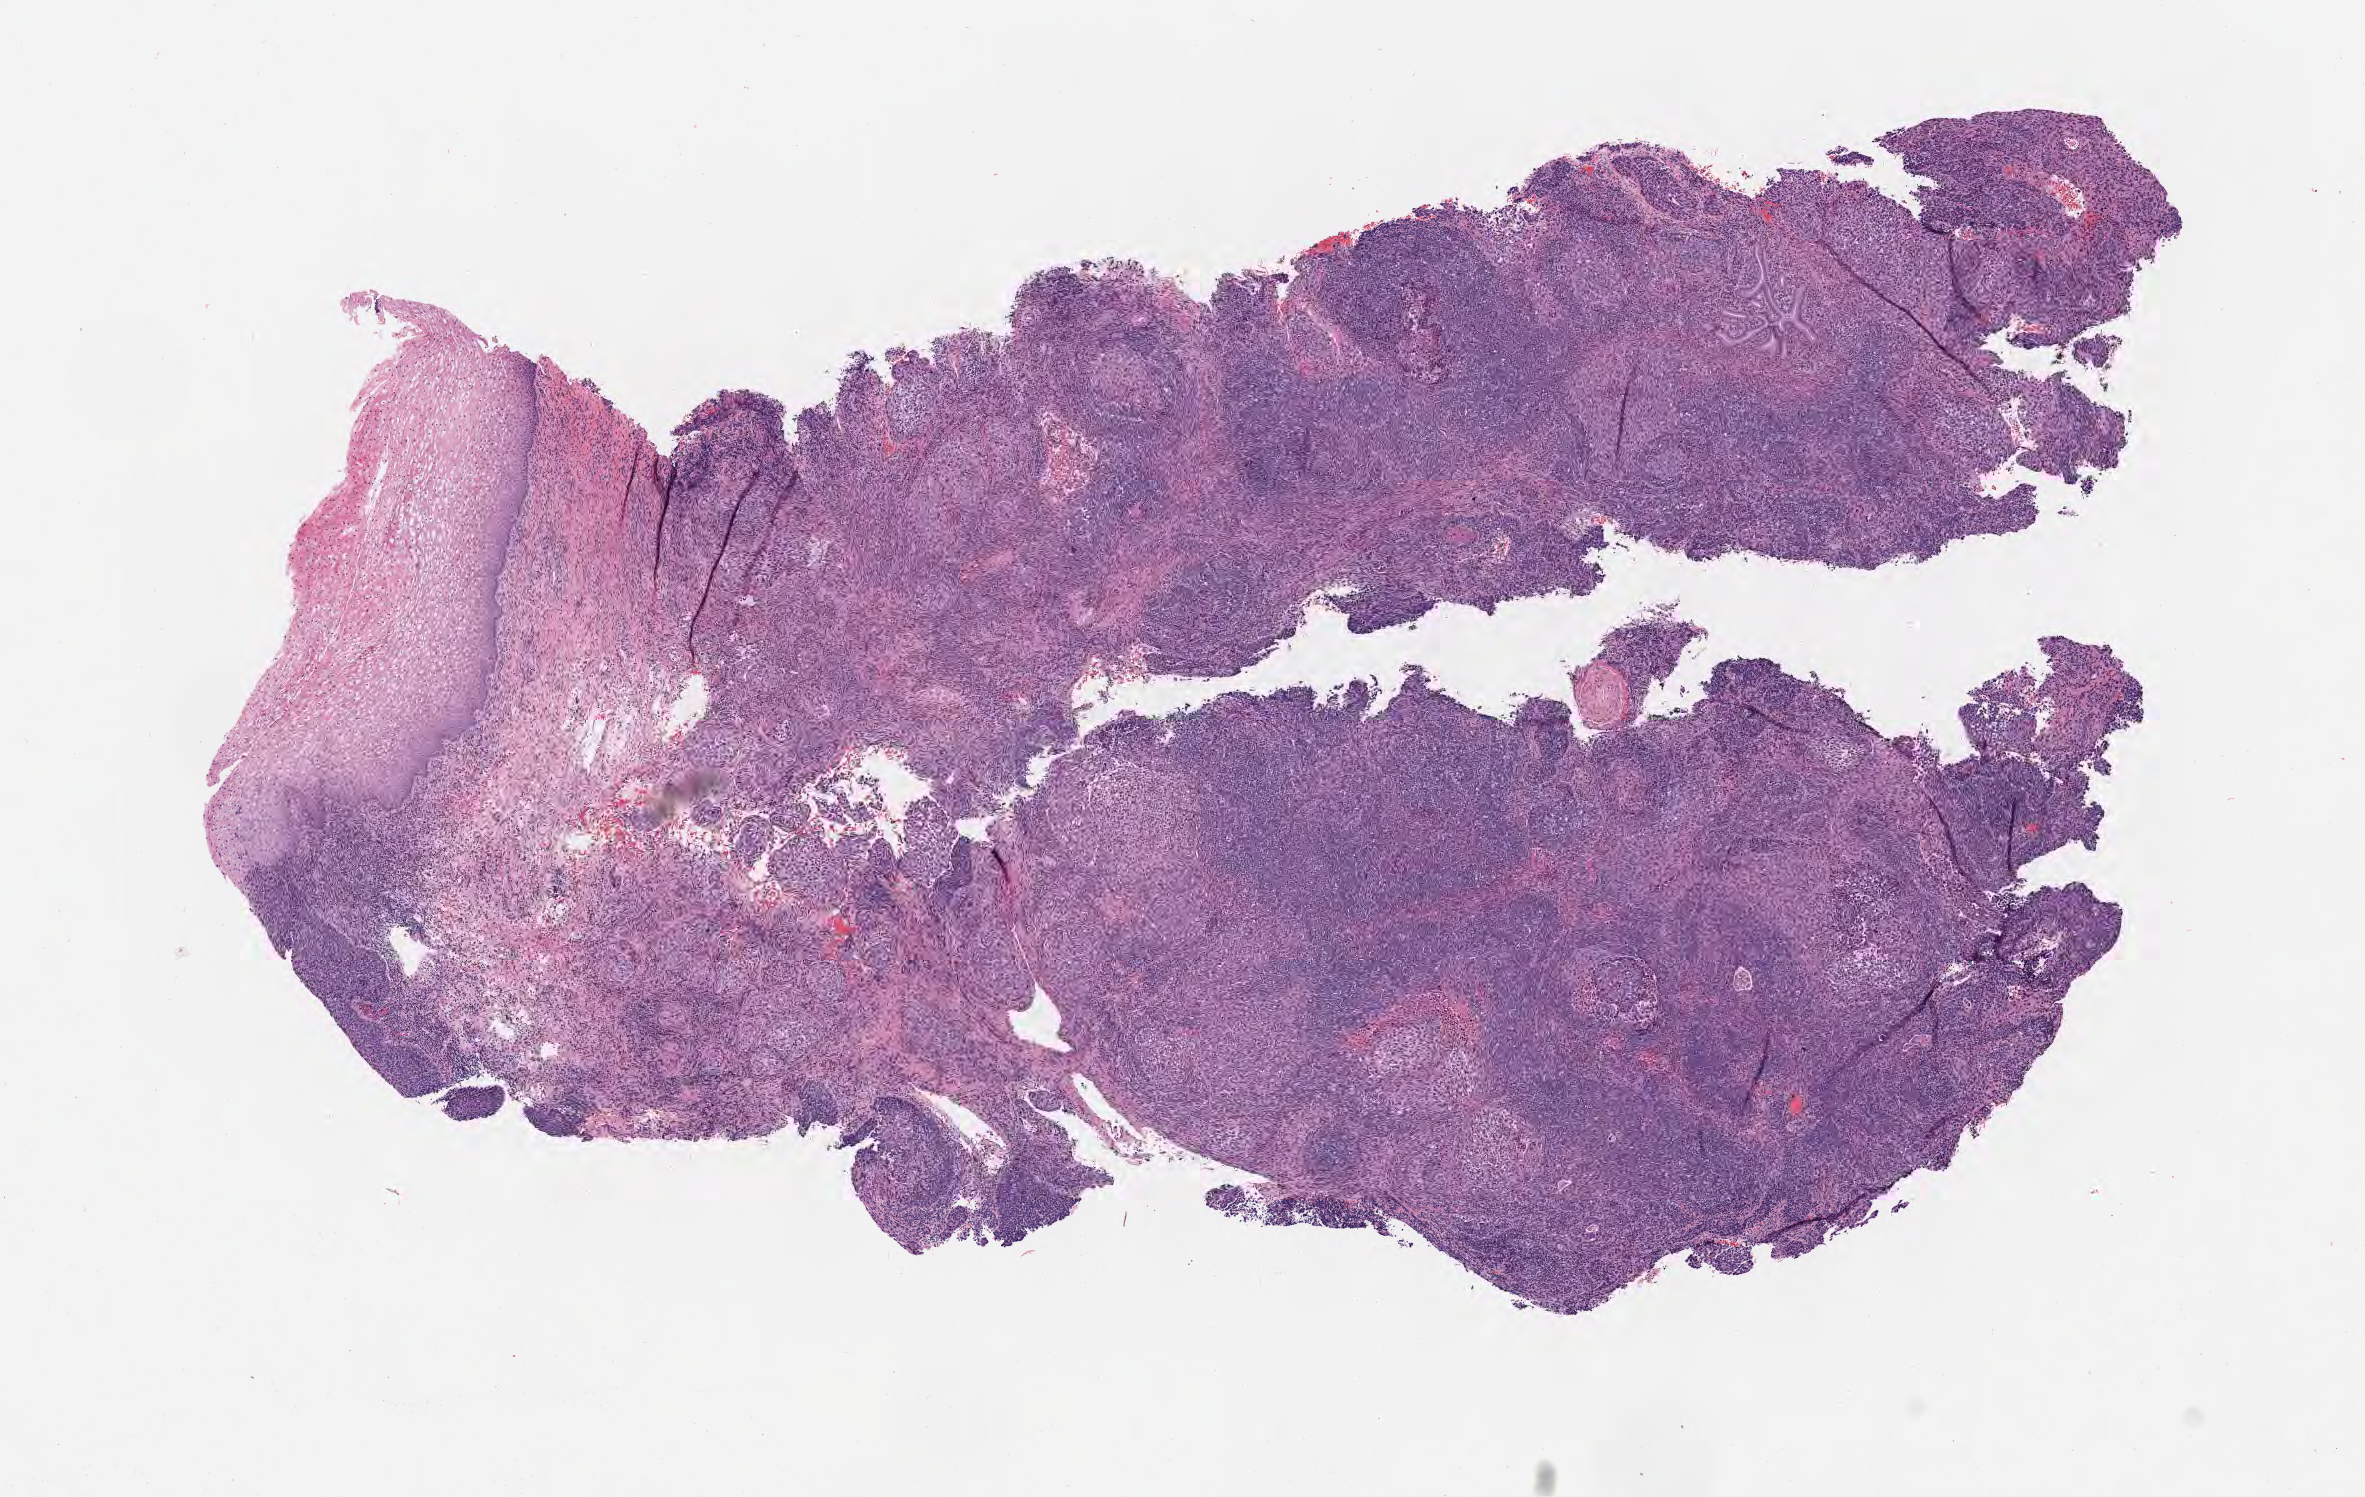
Digitized haematoxylin and eosin-stained section — whole scanned area (about 9.6 x 6.1 mm) shown as a low-resolution overview; tumor tissue; site: cervix. Female patient, 53 years old.
Diagnosis: Squamous cell carcinoma, large cell, nonkeratinizing, NOS.